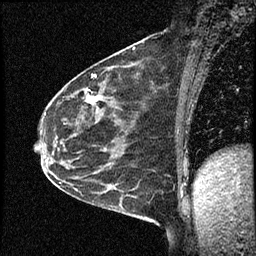
Breast MRI (dynamic contrast-enhanced), one sagittal slice. Dynamic contrast-enhanced study with each time point stored as its own series, time point 2 of 4 at this slice position (early post-contrast, ordered by acquisition time). 1.5 T. TE 4.2 ms, TR 17.6 ms. 2 mm slice thickness. 256 × 256 image matrix. Patient: female, 53 years. Case-level facts recorded for this patient, not image findings: setting: breast cancer imaged before/during neoadjuvant chemotherapy; receptor status: HR-positive, HER2-negative.
Outlined on this slice (semi-automatic segmentation, software-assisted and operator-edited):
- analysis volume of interest (the breast-tissue region the enhancement analysis was run in; not a lesion): bounding box (x1, y1, x2, y2) in pixels: (42, 69, 156, 199)
- tumour enhancement mask (voxels above the 100 % enhancement threshold inside the analysis volume of interest): (88, 96, 100, 104)